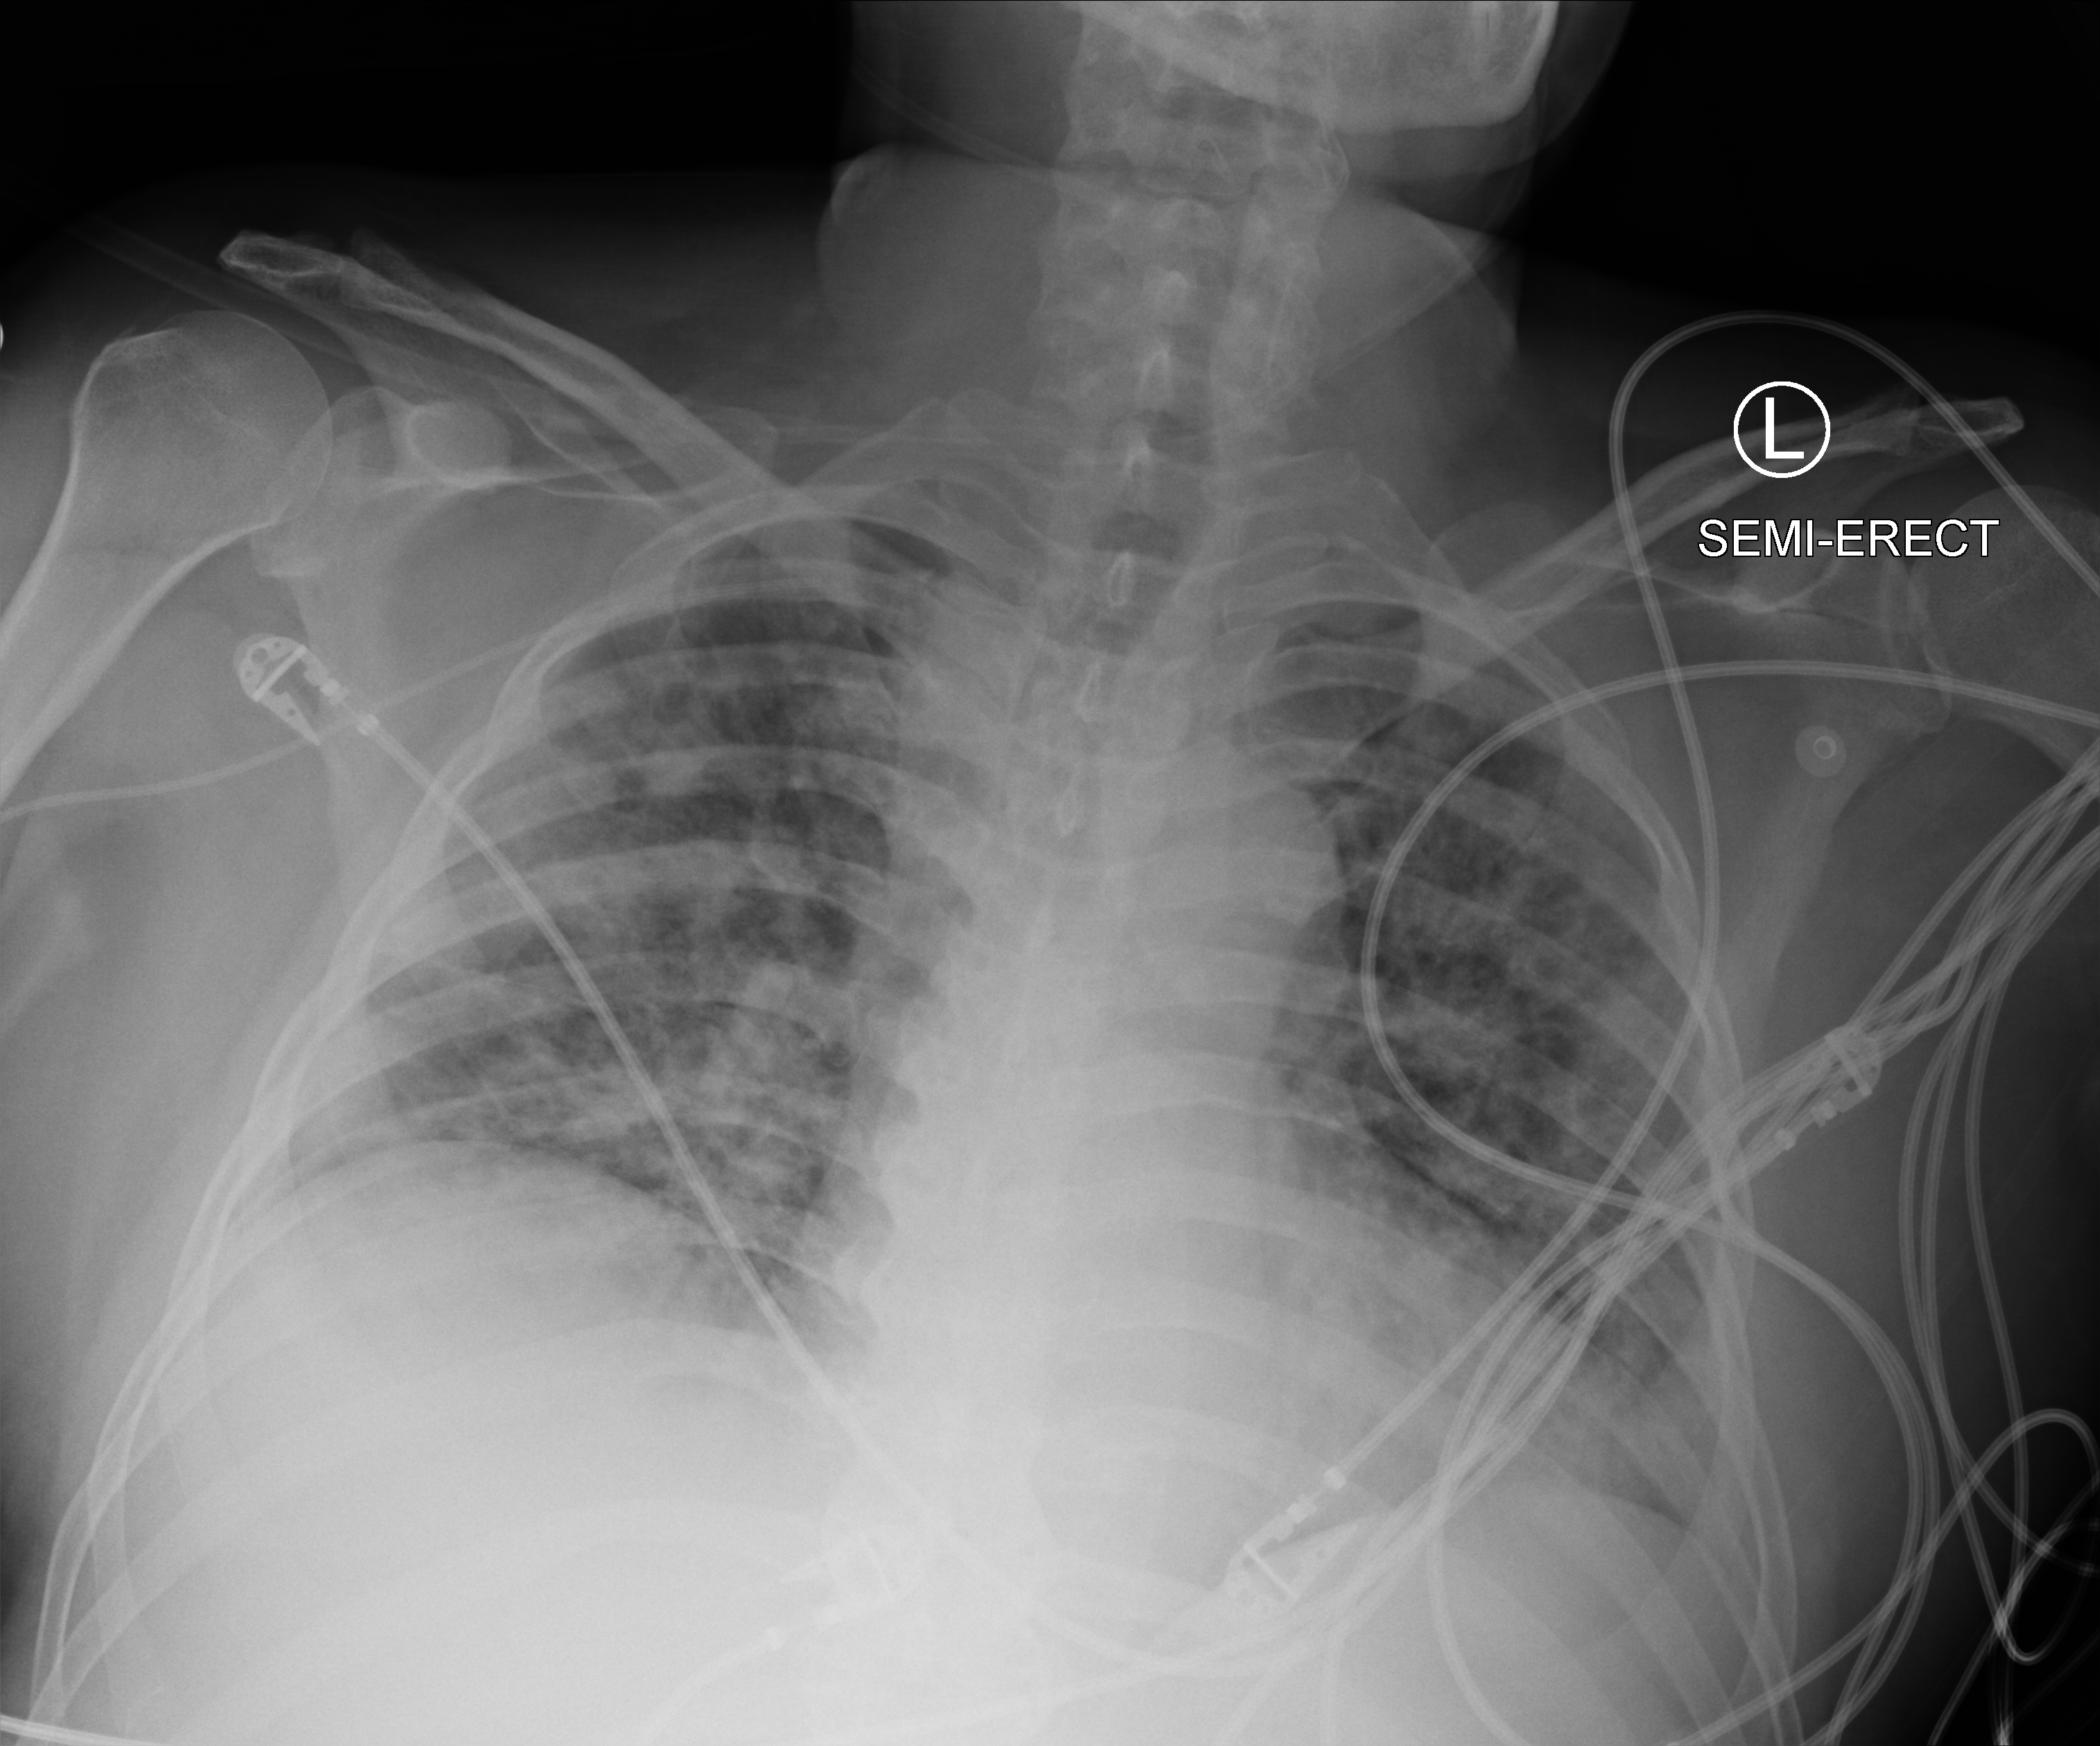
Portable chest radiograph, anteroposterior (AP) projection. Male patient hospitalised with COVID-19, age 18–59 years.
From the hospital-stay record, not from the radiograph (when in the stay this image was taken is not recorded): COPD (admission record): no; hypertension (admission record): yes.